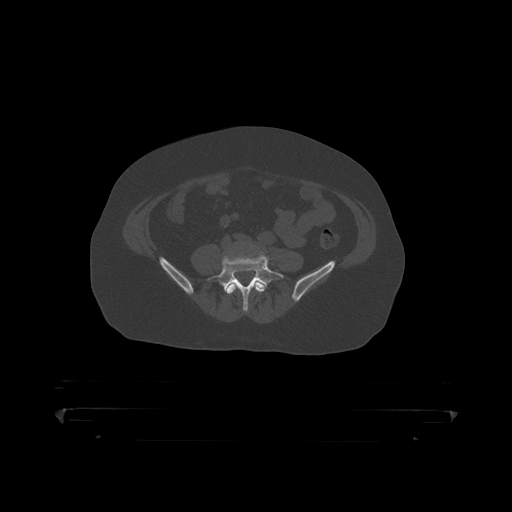
CT including the spine, one axial slice. Position 46 of 390 along the scan axis. Bone window (W 1800 / L 400 HU). 512 × 512 image matrix, field of view 650 × 650 mm. Patient: male, 60 years. Case-level facts recorded for this patient, not image findings: primary cancer: prostate.
Structures marked on this image (semi-automatically segmented with operator editing):
- L4 vertebra: box from (x=226, y=281) to (x=265, y=295) px
- L5 vertebra: (x=208, y=256)–(x=284, y=312)